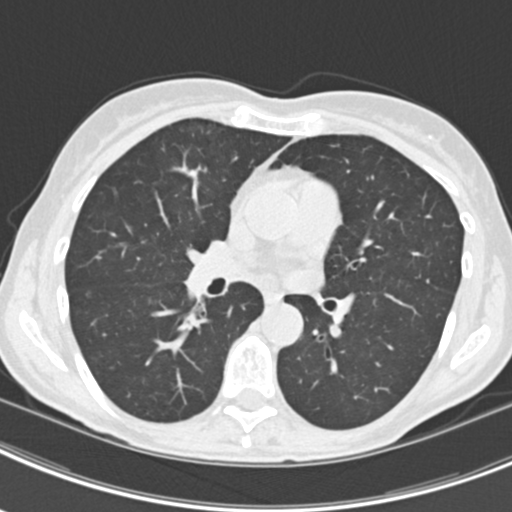
Chest CT (low-dose screening protocol), one axial image, second annual screen, lung window (W 1500 / L -600 HU), 2 mm slice thickness, standard (soft-tissue) reconstruction kernel (B30f), slice 91 of 219 in the series. Female participant, aged 63 years at enrolment. Current smoker at enrolment.
- Expert-annotated lung lesion, box from (x=162, y=148) to (x=224, y=200) px.
- The screening reader recorded 9 non-calcified nodules or masses ≥4 mm on this exam; which of them this box marks is not recorded.
- Official screen result: positive, other.
- Participant outcome: lung cancer diagnosed 408 days after this screen — bronchiolo-alveolar adenocarcinoma, NOS, right upper lobe, right middle lobe, right lower lobe, left upper lobe, left lower lobe, moderately differentiated (G2), stage IV (AJCC 6th edition).